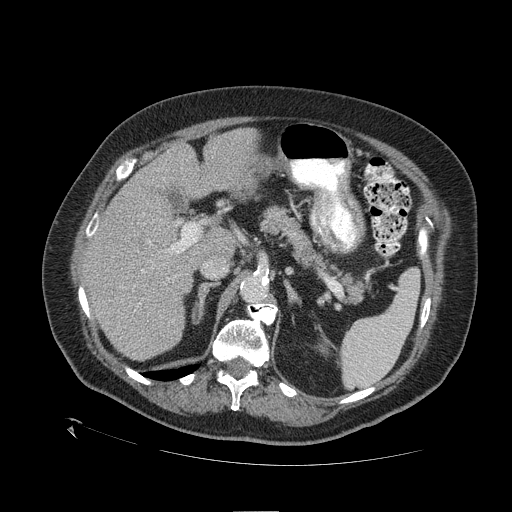
Contrast-enhanced abdominal CT (liver protocol), one axial slice; slice 68 of 109 in the series (ordered by position); one of 2 acquisitions stored at this slice position; soft-tissue window (W 400 / L 40 HU); 2.5 mm slice thickness; 512 × 512 image matrix, field of view 460 × 460 mm. From the clinical record (not read from this slice): diagnosis: hepatocellular carcinoma (patient treated with transarterial chemoembolisation; whether this scan precedes or follows treatment is not stated here); TNM stage (as recorded): Stage-I; Child-Pugh class: A; tumour differentiation: no biopsy; tumour nodularity: uninodular.
Outlined on this slice (semi-automatically segmented with operator editing):
- liver parenchyma outside the tumour (the mass and vessels are separate outlines, so this box may not span the whole liver): bounding box <82,128,256,360> (left, top, right, bottom; pixels)
- liver vessels: <89,225,185,279>